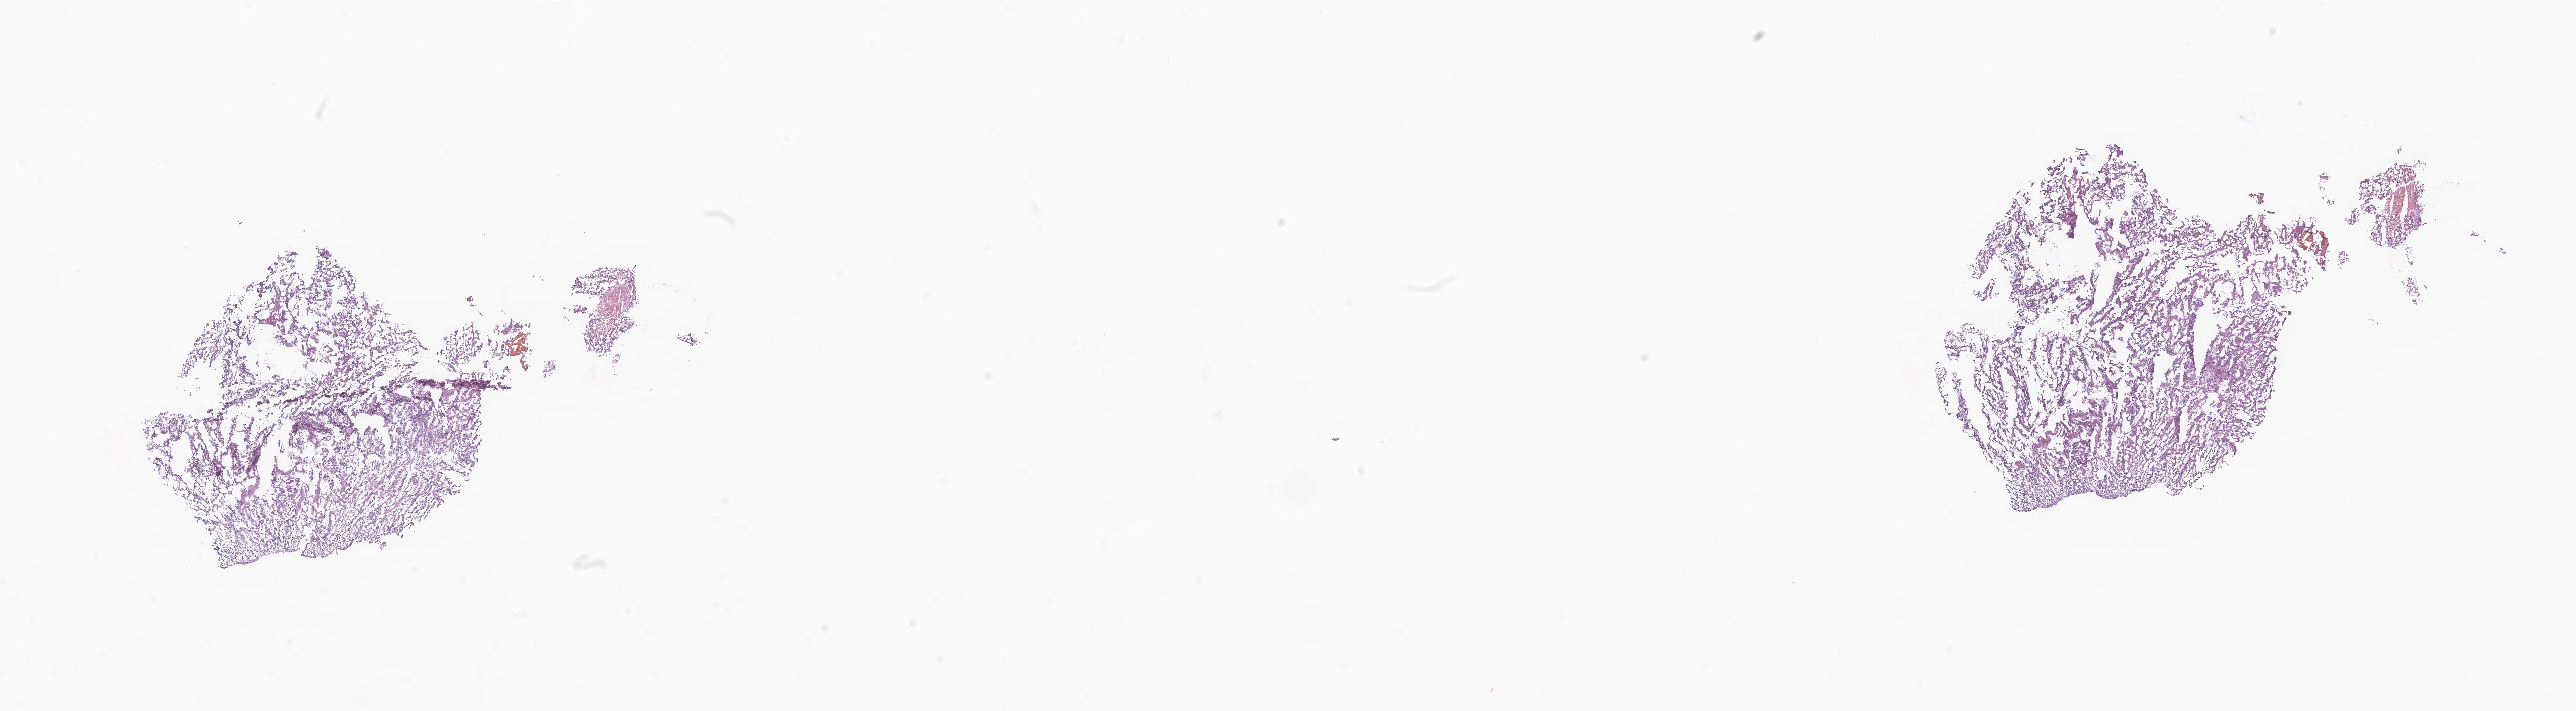
Digitized haematoxylin and eosin-stained section of tumor tissue from the central nervous system — low-resolution overview of the scanned area, about 33.4 x 9.2 mm, frozen section (OCT-embedded). Female patient, age 144 months (12 years).
Diagnosis: Ependymoma, NOS.